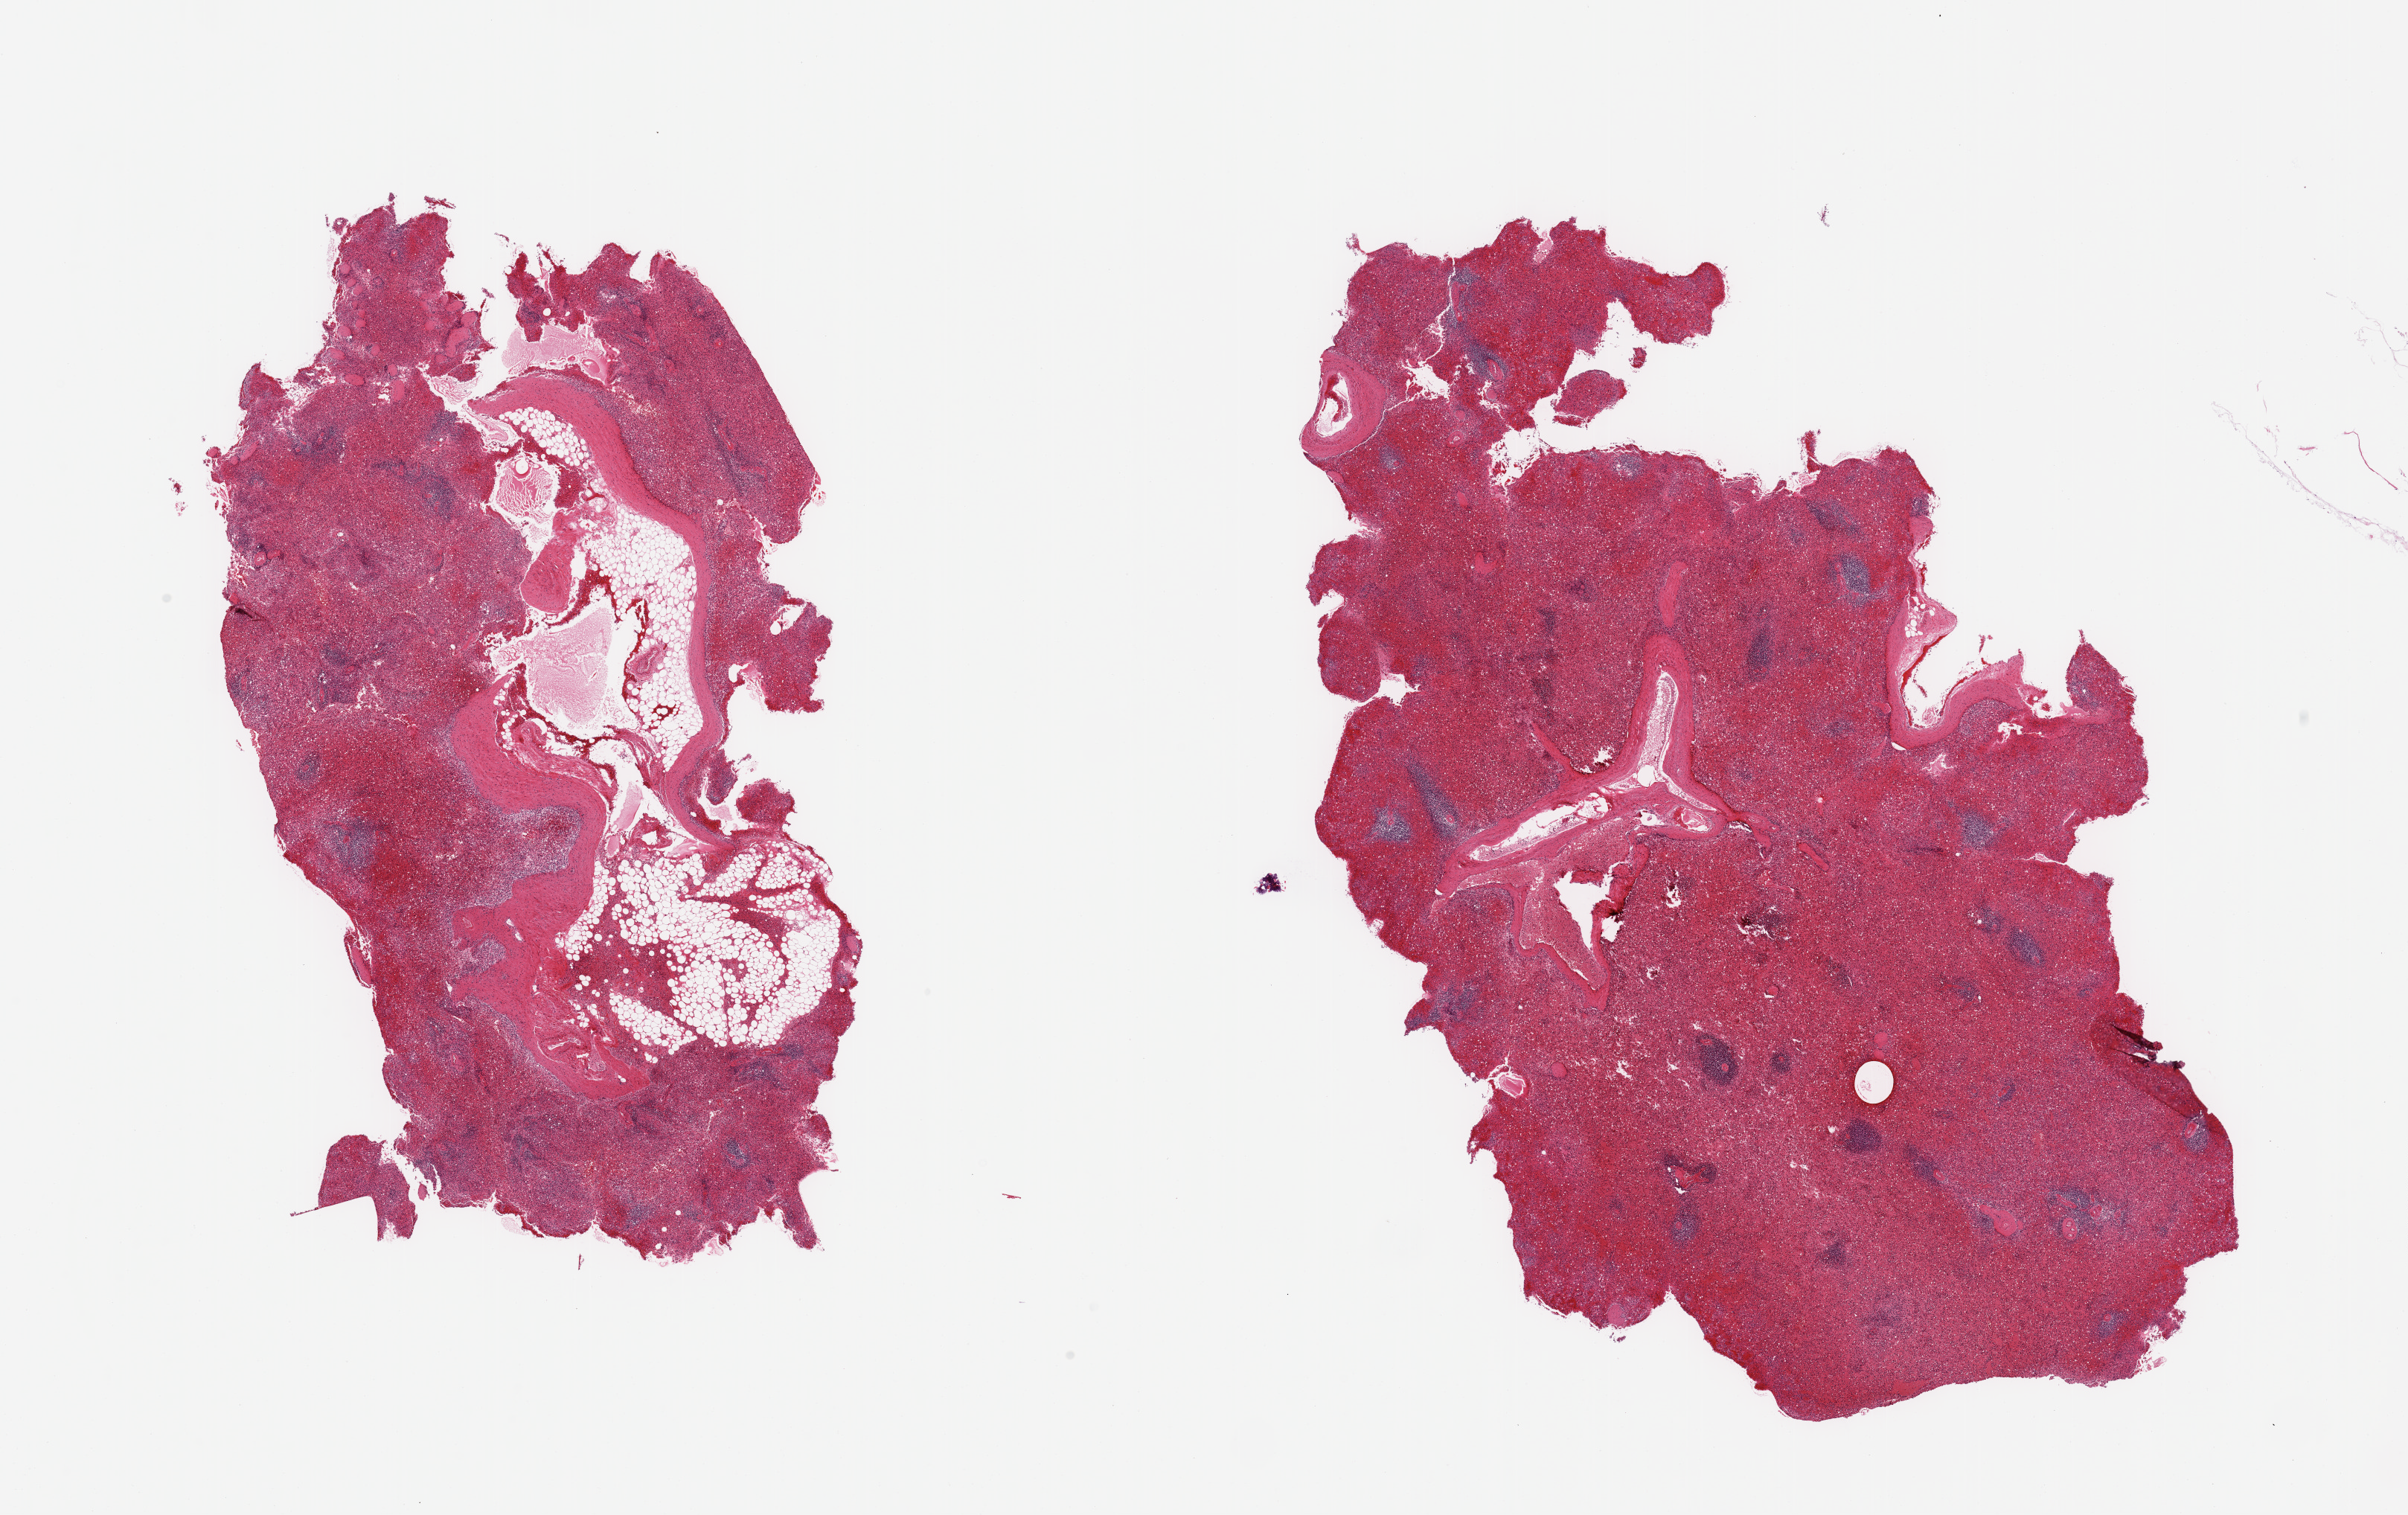
Whole-slide image, H&E stain, brightfield — whole scanned area (about 25.6 x 16.1 mm) shown as a low-resolution overview, PAXgene-fixed paraffin-embedded (PFPE) section, sampled site (target tissue): spleen, tissue donor sample. Donor sex: female.
* pathologist's review note for this sample: 2 pieces; congestion, one piece includes ~10% fat